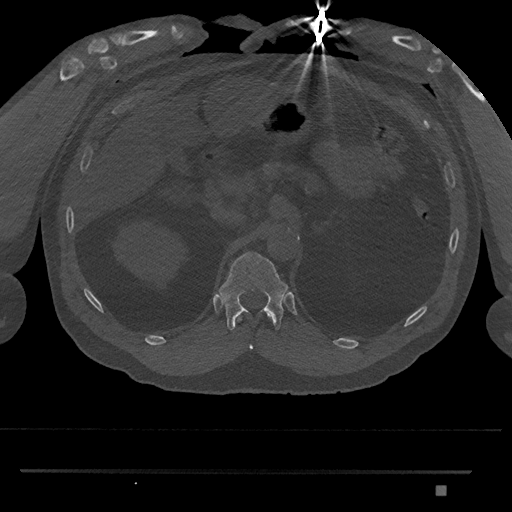
CT including the spine, one axial slice; slice 903 of 1134 in the series (ordered by position); bone window (W 1800 / L 400 HU); 0.5 mm slice thickness; 512 × 512 image matrix. Patient: male, 65 years. From the clinical record (not read from this slice): primary cancer: prostate.
Annotated regions visible in this slice (semi-automatically segmented with operator editing):
- T11 vertebra: bounding box (x1, y1, x2, y2) in pixels: (238, 314, 270, 350)
- T12 vertebra: (219, 251, 288, 332)